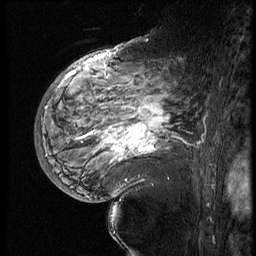
Breast MRI (dynamic contrast-enhanced), one sagittal slice; slice 38 of 60 in the series (ordered by position); 4 images stored at this slice position (order not interpretable as contrast timing); 1.5 T; TE 4.2 ms, TR 9 ms; 2.5 mm slice thickness; 256 × 256 image matrix, field of view 180 × 180 mm. Female patient, age 56 years. From the clinical record (not read from this slice): setting: breast cancer imaged before/during neoadjuvant chemotherapy; receptor status: HER2-positive.
Annotated regions visible in this slice (semi-automatically segmented with operator editing):
- analysis volume of interest (the breast-tissue region the enhancement analysis was run in; not a lesion): bounding box (x1, y1, x2, y2) in pixels: (82, 83, 199, 177)
- tumour enhancement mask (voxels above the 140 % enhancement threshold inside the analysis volume of interest): (104, 102, 169, 162)